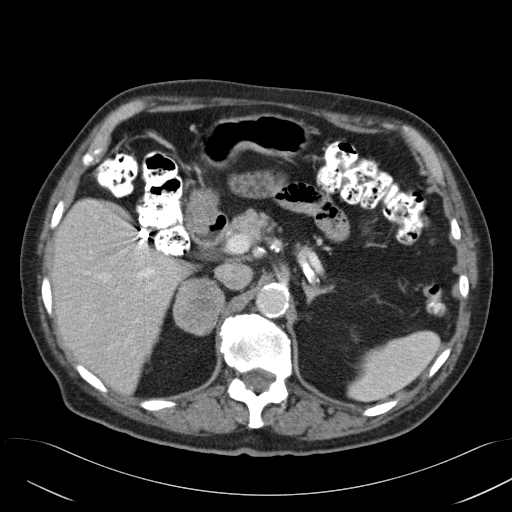
Contrast-enhanced abdominal CT, one axial slice. Position 32 of 58 along the scan axis. Reconstruction kernel B31f. 120 kVp. Intravenous contrast given. Soft-tissue window (W 400 / L 40 HU). 512 × 512 image matrix, field of view 384 × 384 mm. Patient: male, 82 years. Case-level facts recorded for this patient, not image findings: diagnosis: adrenocortical carcinoma; tumour side: right adrenal; tumour size at pathology: 9 cm; Ki-67 index: 30 %; stage (as recorded): 3.
Outlined on this slice (semi-automatic segmentation, software-assisted and operator-edited):
- mass: bounding box (x1, y1, x2, y2) in pixels: (174, 285, 222, 332)